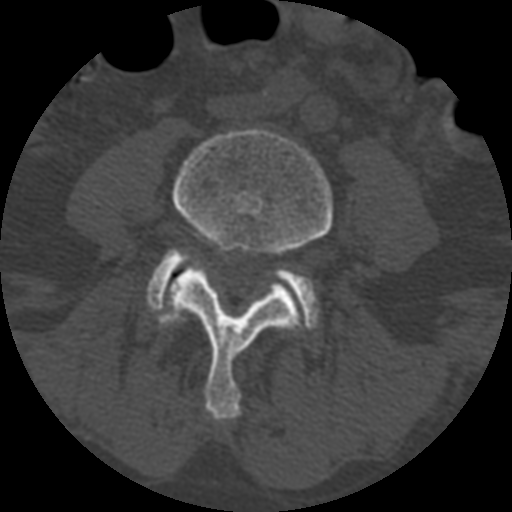
CT including the spine, one axial slice; position 275 of 399 along the scan axis; reconstruction kernel STANDARD; bone window (W 1800 / L 400 HU); 1.25 mm slice thickness; 512 × 512 image matrix. Patient age 71 years. Case-level facts recorded for this patient, not image findings: primary cancer: prostate.
Structures marked on this image (semi-automatically segmented with operator editing):
- L4 vertebra: bounding box <157,129,333,420> (left, top, right, bottom; pixels)
- L5 vertebra: <145,249,319,332>